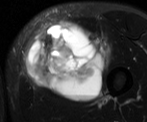
MRI of an extremity soft-tissue mass, one axial slice. Slice 25 of 52 in the series (ordered by position). T2-weighted fat-saturated. MR volume resampled by the dataset authors to the PET/CT grid (not the native acquisition matrix). 3.27 mm slice thickness. 147 × 122 image matrix, field of view 144 × 119 mm. Male patient. Case-level facts recorded for this patient, not image findings: histological type: pleiomorphic liposarcoma; grade: high; site of the primary tumour: left thigh.
Annotated regions visible in this slice (expert contour drawn on MRI and transferred to this co-registered scan by the dataset authors):
- gross tumour volume including surrounding oedema: bounding box [x1, y1, x2, y2] px = [23, 18, 113, 102]
- gross tumour volume (mass): [23, 18, 108, 102]